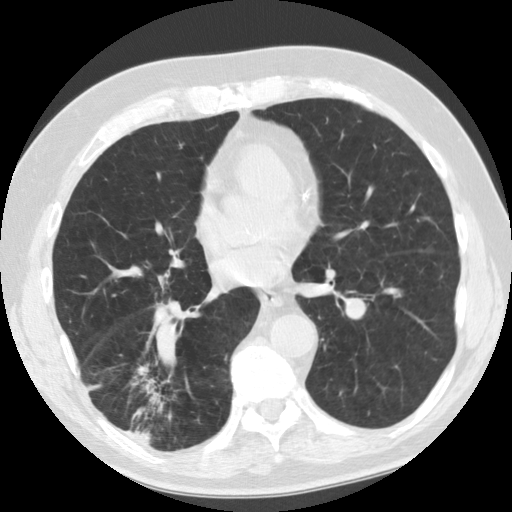
Low-dose screening chest CT, one axial slice. Slice 55 of 135 in the series (ordered by position). Reconstruction kernel STANDARD. 120 kVp. Lung window (W 1500 / L -600 HU). 512 × 512 image matrix, field of view 340 × 340 mm.
Structures marked on this image (expert manual segmentation):
- lesion 1 (tumor, lower lobe of right lung): box from (x=137, y=365) to (x=172, y=418) px